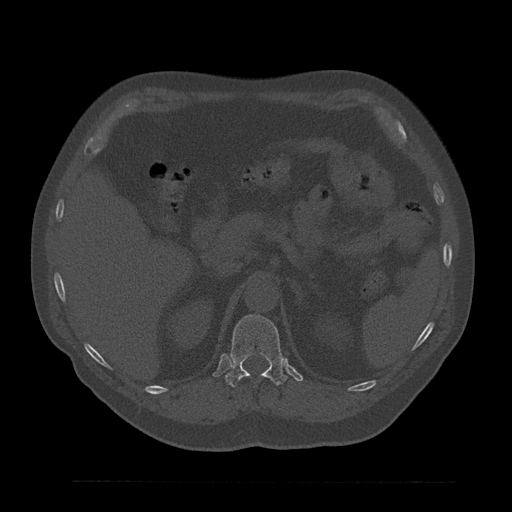
CT including the spine, one axial slice. Slice 238 of 797 in the series (ordered by position). Reconstruction kernel Br40s/3. 120 kVp. Bone window (W 1800 / L 400 HU). 0.5 mm slice thickness. 512 × 512 image matrix, field of view 430 × 430 mm. Patient: male, 61 years. From the clinical record (not read from this slice): primary cancer: prostate.
Outlined on this slice (semi-automatically segmented with operator editing):
- T12 vertebra: box from (x=225, y=314) to (x=287, y=388) px